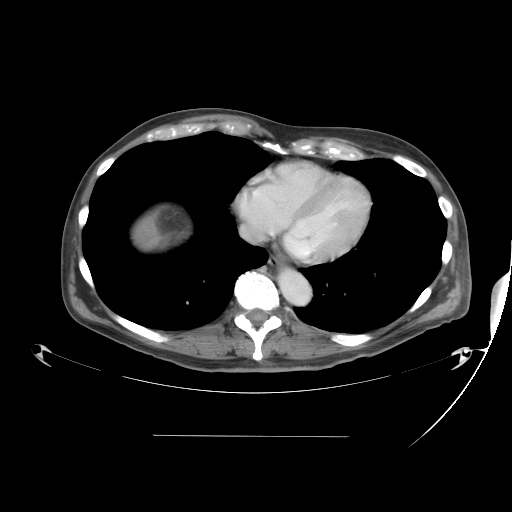
Contrast-enhanced abdominal CT, one axial slice; slice 43 of 48 in the series (ordered by position); reconstruction kernel STANDARD; 120 kVp; intravenous contrast given; soft-tissue window (W 400 / L 40 HU); 512 × 512 image matrix, field of view 486 × 486 mm. Male patient, age 65 years. Case-level facts recorded for this patient, not image findings: diagnosis: colorectal cancer liver metastases, imaged before liver resection; multiple liver metastases: yes; largest metastasis: 11 cm; chemotherapy before resection: yes.
Annotated regions visible in this slice (expert manual segmentation):
- liver: bounding box (x1, y1, x2, y2) in pixels: (132, 219, 157, 251)
- liver metastasis: (130, 218, 156, 250)